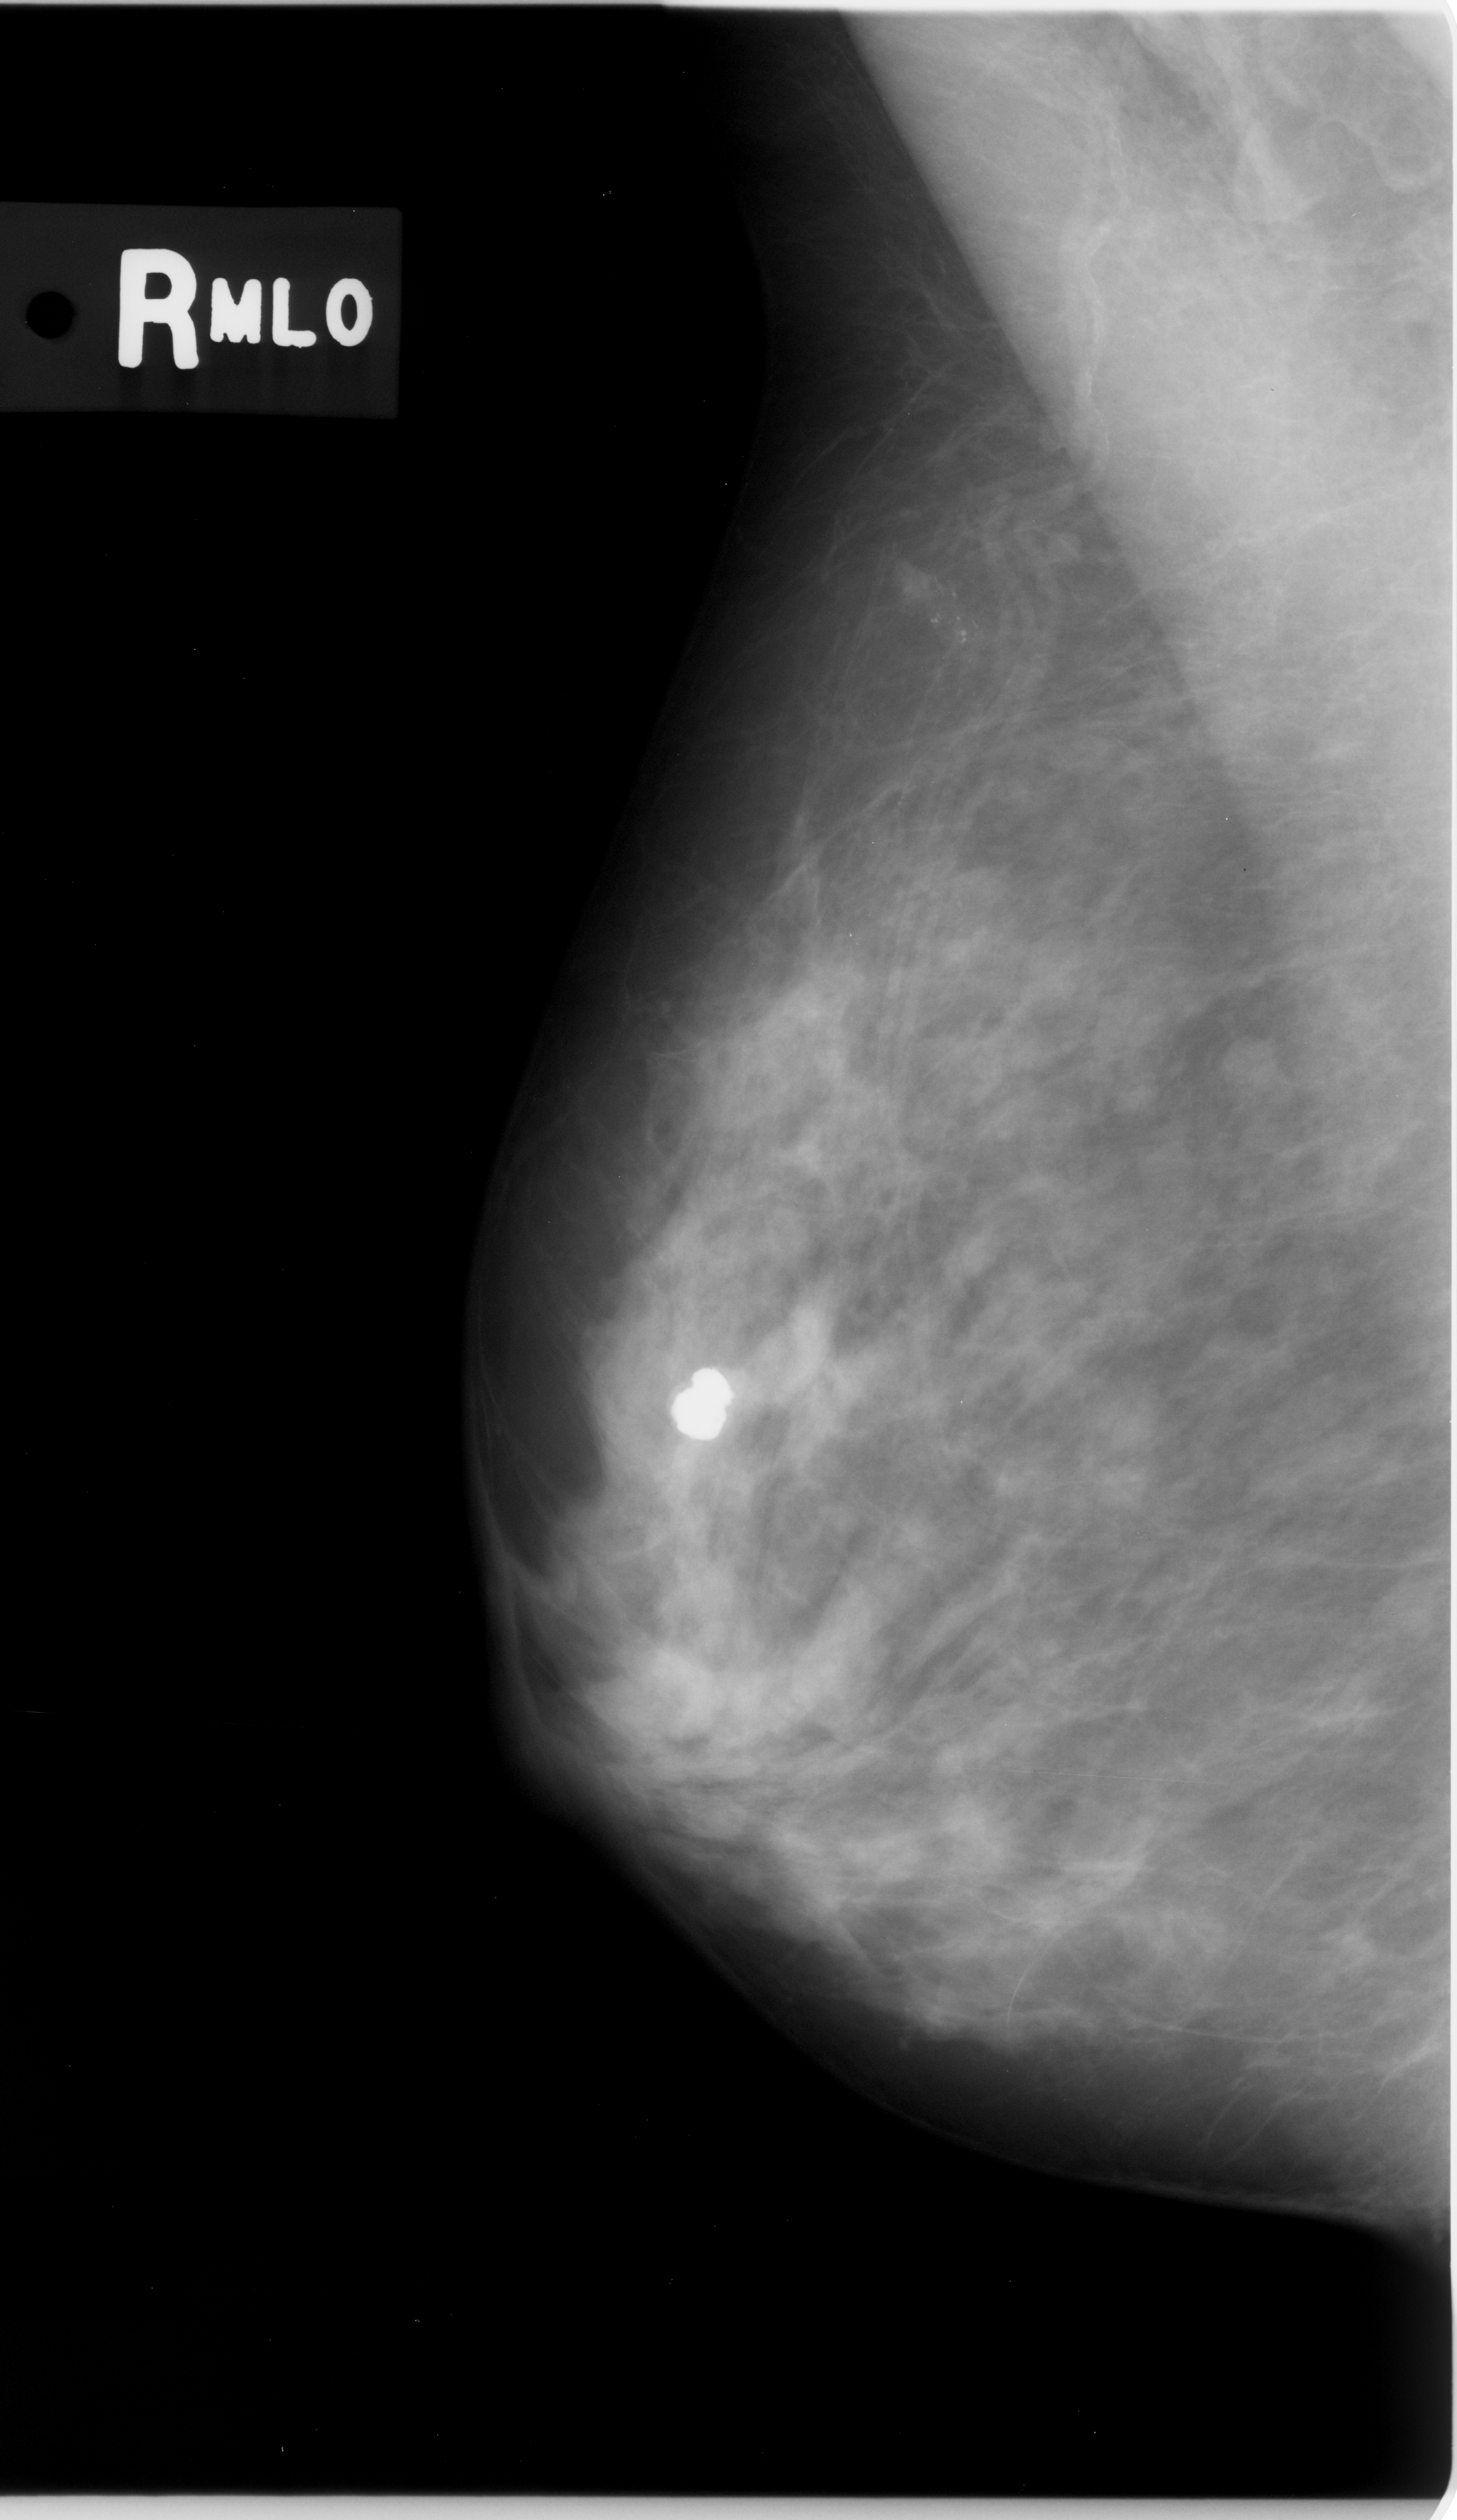
Scanned film-screen mammogram, right breast, MLO view, BI-RADS breast density category 3 (scale 1–4).
Marked abnormality: calcifications, morphology pleomorphic, distribution clustered; BI-RADS assessment category 5; pathology (as recorded): malignant.